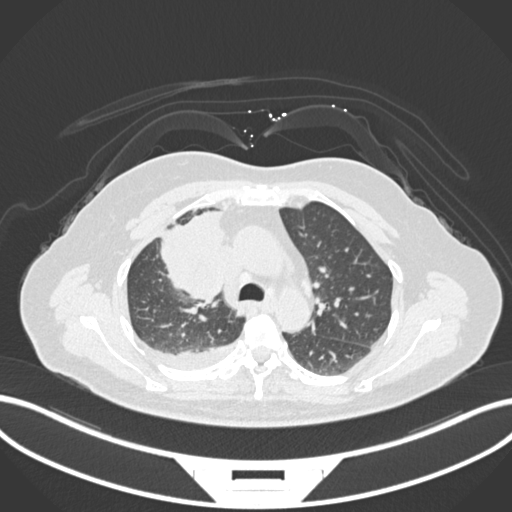
Chest CT, one axial slice. Slice 106 of 172 in the series (ordered by position). Reconstruction kernel B30f. 120 kVp. Lung window (W 1500 / L -600 HU). 1 mm slice thickness. 512 × 512 image matrix, field of view 400 × 400 mm. Female patient, age 52 years. Case-level facts recorded for this patient, not image findings: clinical TNM (as recorded): T3 N1 M1.
Outlined on this slice (rectangle marked by the reading radiologist):
- lung tumour (recorded histology: adenocarcinoma): bounding box <159,212,230,307> (left, top, right, bottom; pixels)